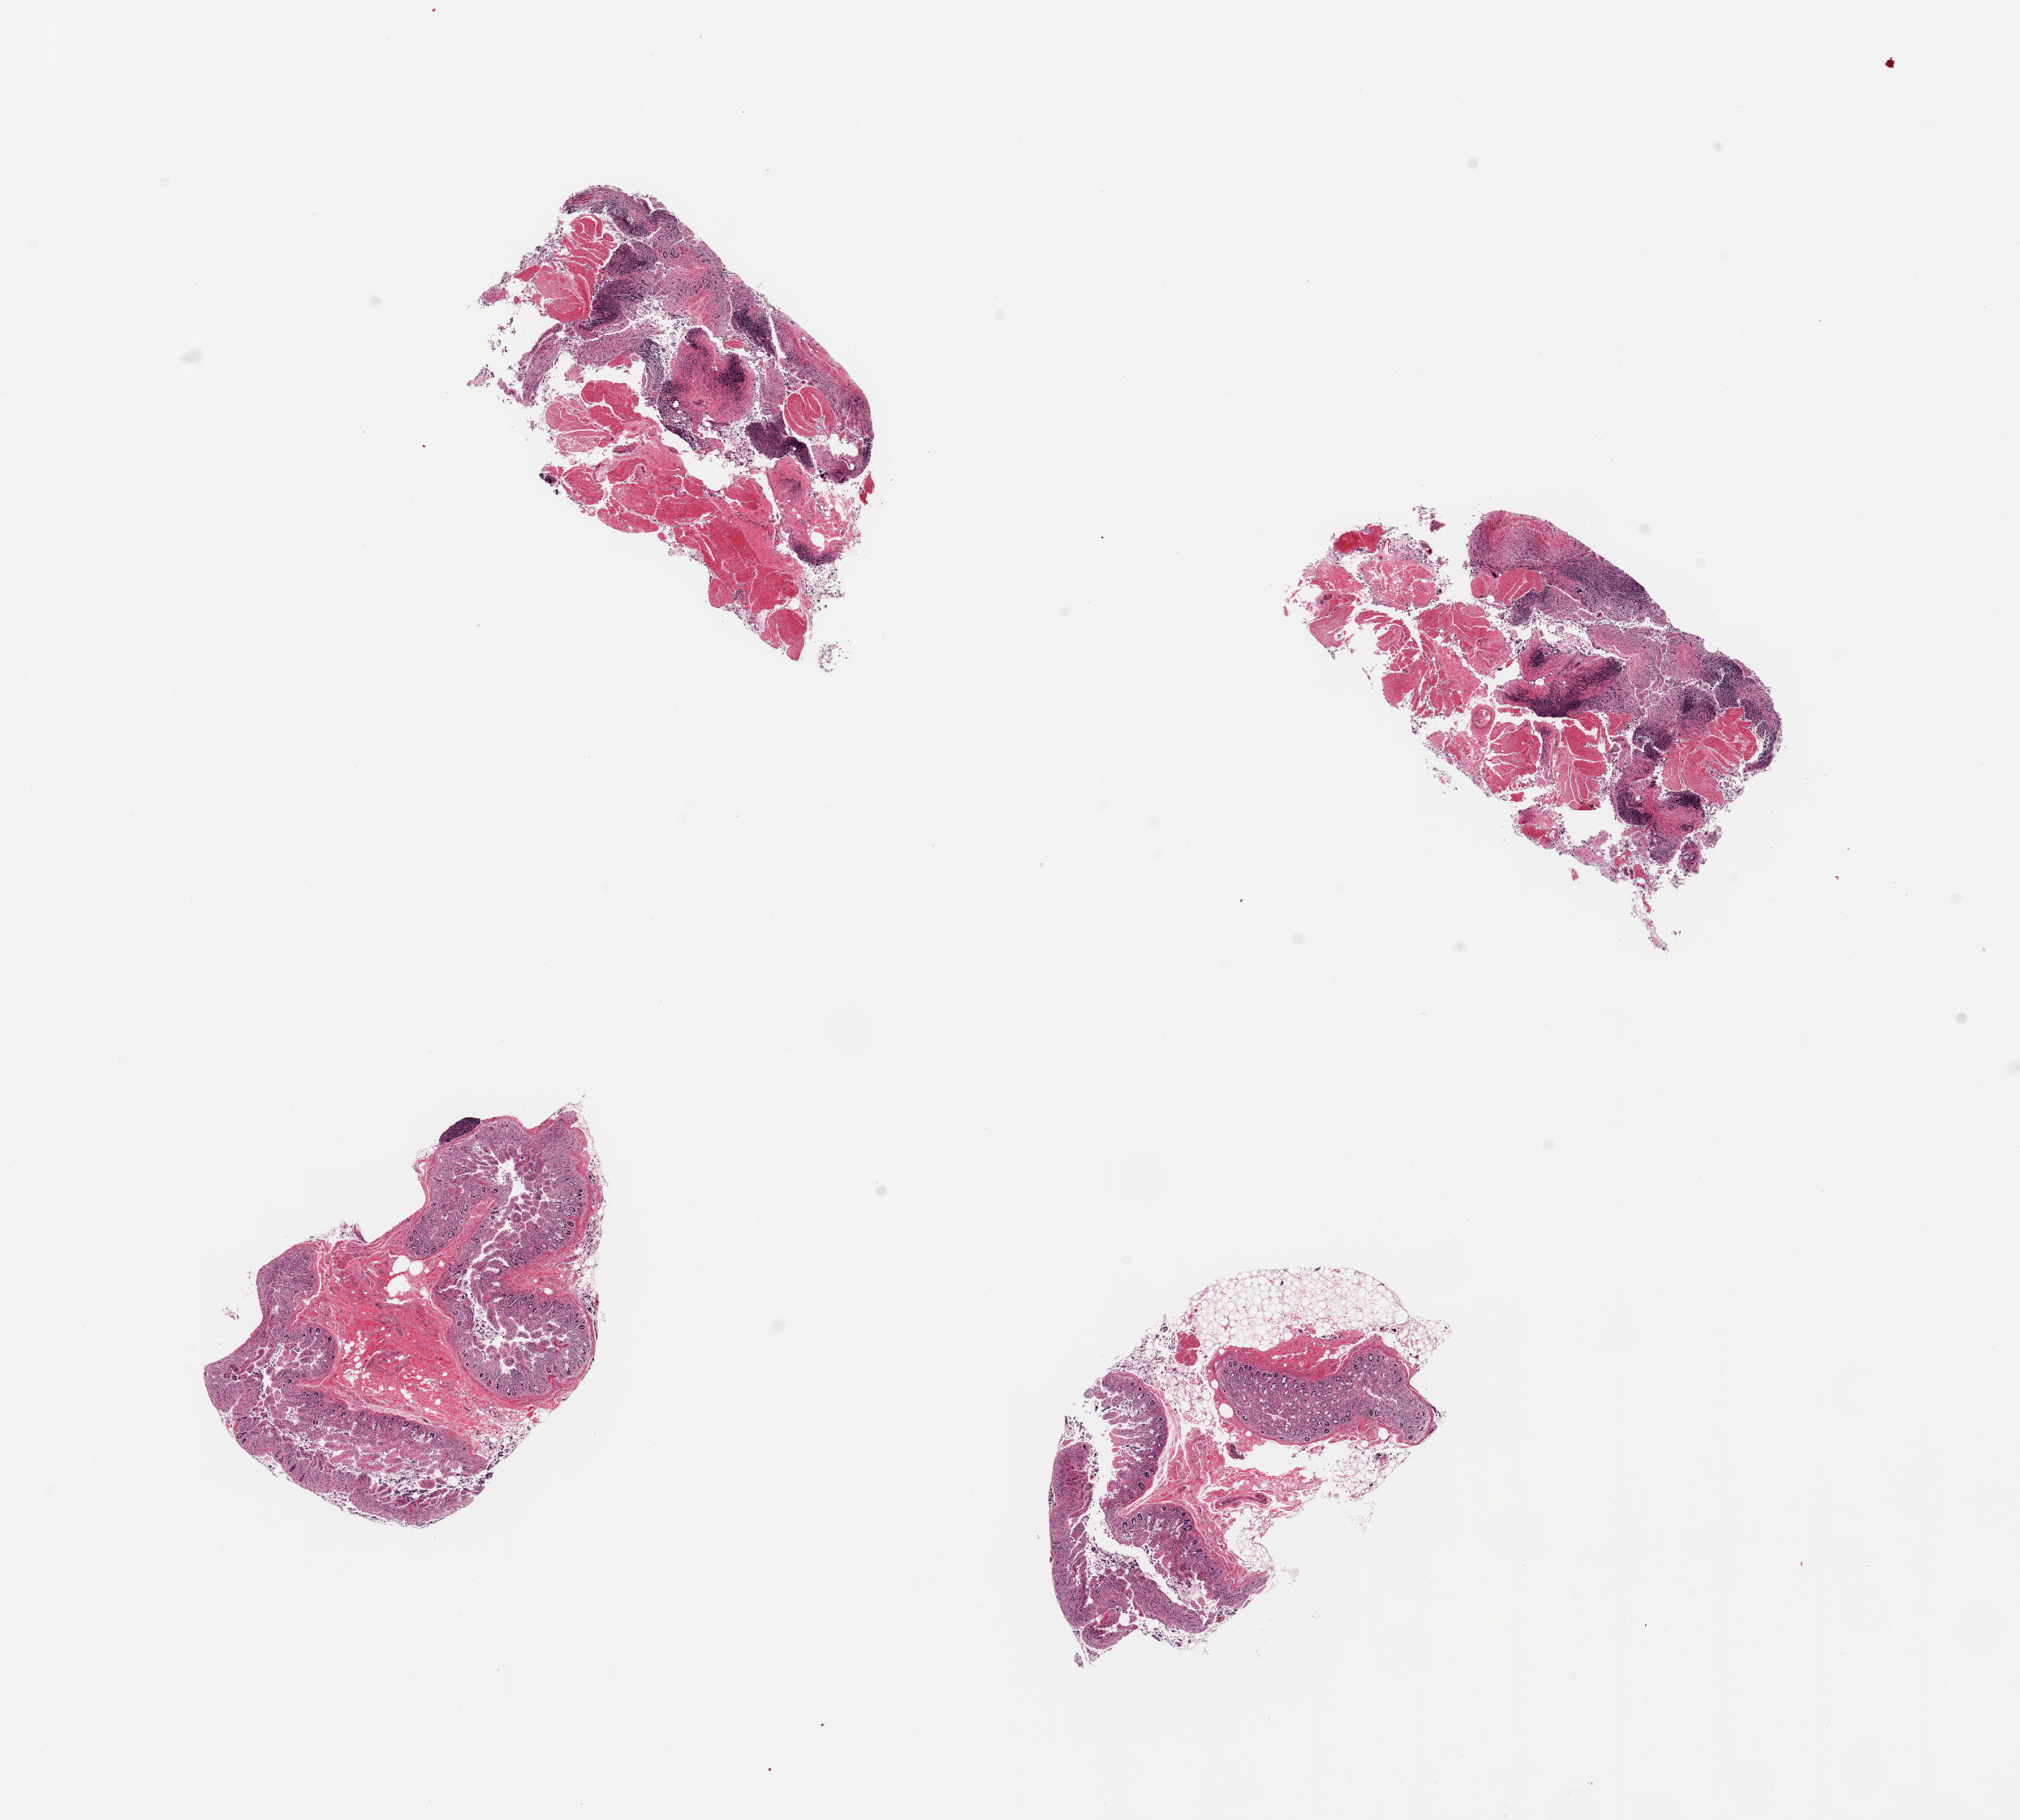
Hematoxylin and eosin (H&E) whole-slide image, whole scanned area (about 19.7 x 17.7 mm, slide scanned at 20x) shown as a low-resolution overview, PAXgene-fixed paraffin-embedded (PFPE) section, target tissue: ileum, donor tissue sample.
* pathologist's review note for this sample: 4 pieces, mucosa autolyzed, lymphoid aggregates ~10-15% total